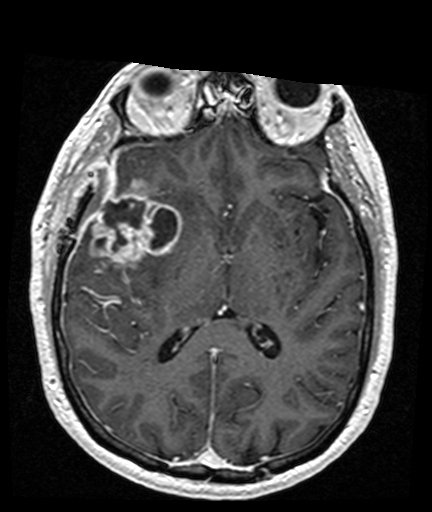
Brain MRI from a brain-tumour surgery series, one axial slice; slice 82 of 176 in the series (ordered by position); T1-weighted post-contrast; 1 mm slice thickness; 432 × 512 image matrix, field of view 194 × 230 mm. Case-level facts recorded for this patient, not image findings: histopathology: Glioblastoma; WHO grade: 4.
Outlined on this slice (expert manual segmentation):
- tumour: box from (x=88, y=180) to (x=182, y=269) px